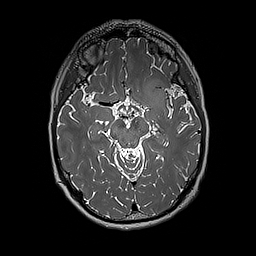
Brain MRI from a brain-tumour surgery series, one axial slice. Position 113 of 192 along the scan axis. 1 mm slice thickness. 256 × 256 image matrix. From the clinical record (not read from this slice): histopathology: Glioblastoma; WHO grade: 4; IDH mutation: no; tumour location: Left Insular.
Annotated regions visible in this slice (manually delineated by an expert):
- tumour: bounding box <140,79,171,112> (left, top, right, bottom; pixels)